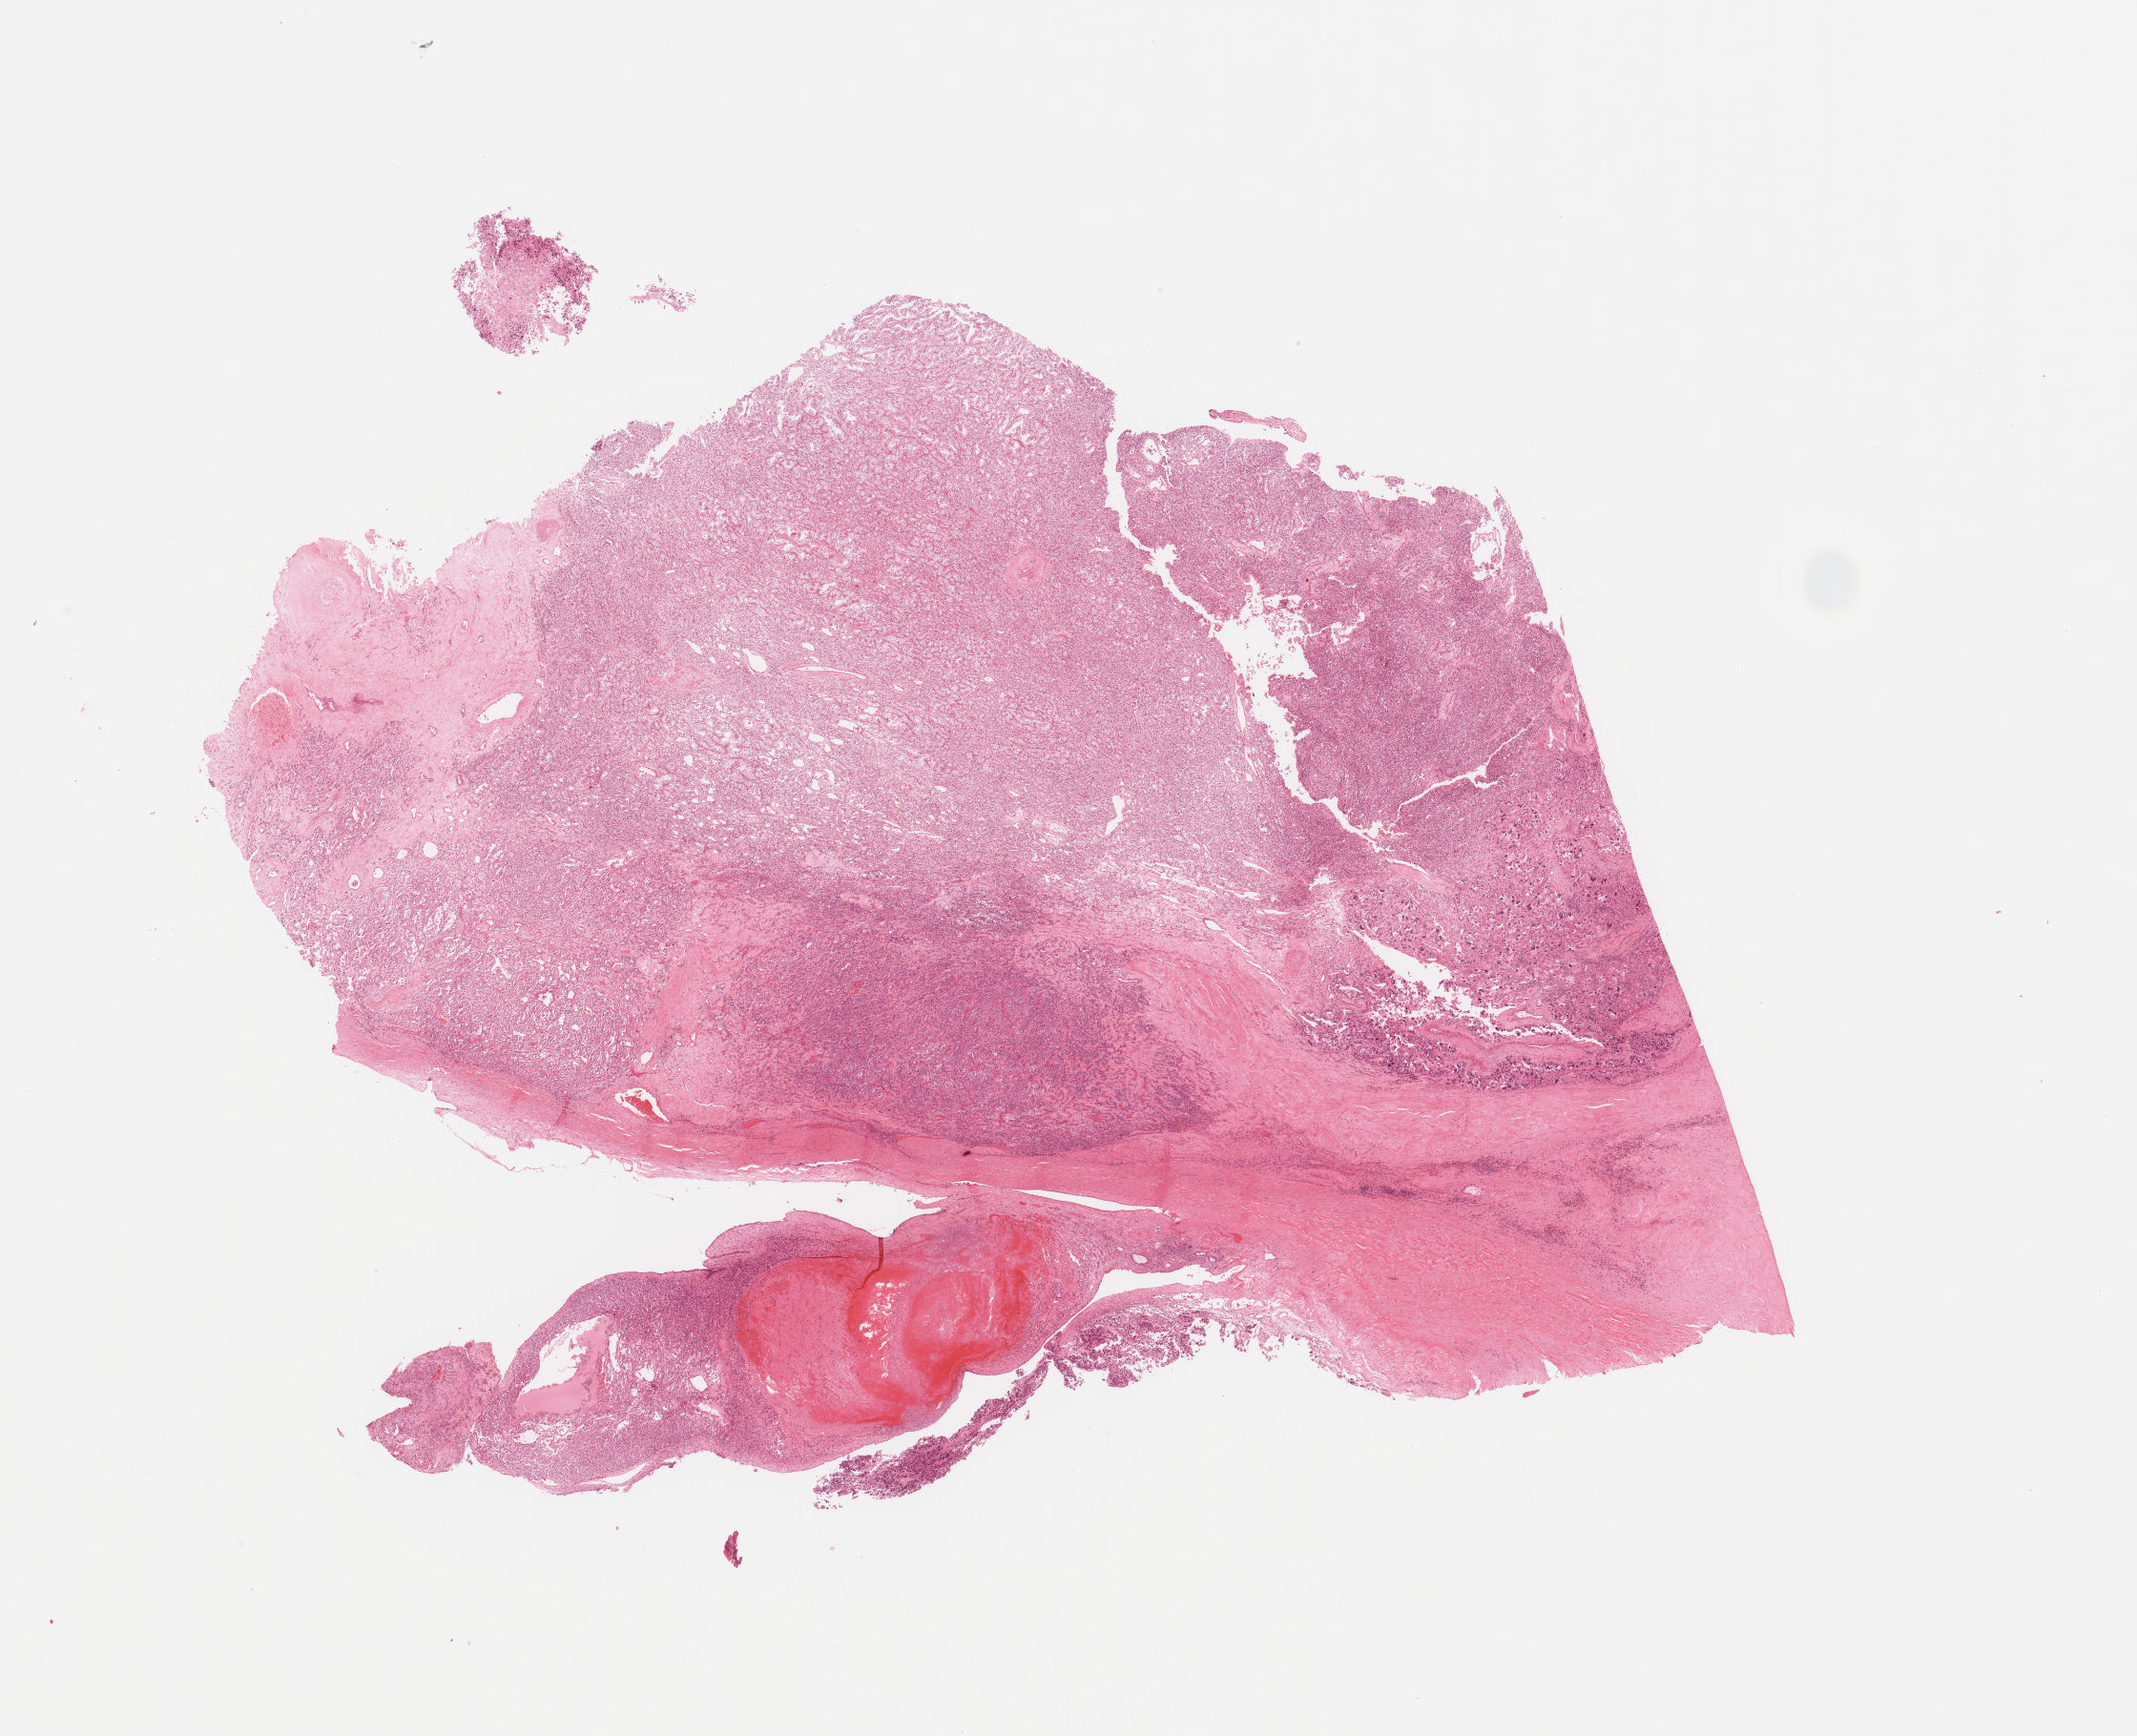
Whole-slide histology image, H&E, whole scanned area (about 17.7 x 14.4 mm) shown as a low-resolution overview; tumour tissue sample, sampled site: kidney. Female, 68 y/o. Histologic grade: G3 (poorly differentiated). Pathologist review of this section (percent, as recorded): tumour nuclei 80%, necrosis 7%.
Histologic diagnosis: Renal cell carcinoma, NOS.